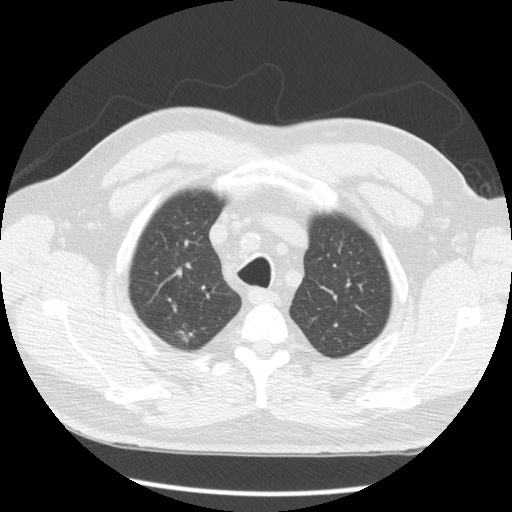
Chest CT (low-dose screening protocol), one axial image, first (baseline) screen, lung window (W 1500 / L -600 HU), 2.5 mm slice thickness, standard (soft-tissue) reconstruction kernel (STANDARD), slice 22 of 163 in the series. Male, age 65 years at enrolment.
Expert reader's lesion annotation, bounding box (x1, y1, x2, y2) in pixels: (158, 318, 207, 360). The exam's reader record, not a measurement of the box and not confirmed to be the same lesion: non-calcified nodule or mass ≥4 mm, right upper lobe, 10 × 9 mm, spiculated (stellate) margins, soft tissue attenuation.